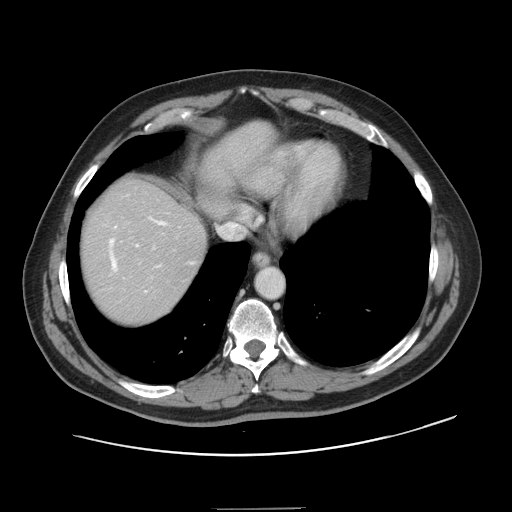
Contrast-enhanced abdominal CT, one axial slice; position 128 of 143 along the scan axis; 120 kVp; soft-tissue window (W 400 / L 40 HU); 2.5 mm slice thickness; 512 × 512 image matrix, field of view 402 × 402 mm. Male patient, age 62 years. Case-level facts recorded for this patient, not image findings: diagnosis: colorectal cancer liver metastases, imaged before liver resection.
Outlined on this slice (outlined manually by an expert reader):
- hepatic veins: bounding box <109,218,191,292> (left, top, right, bottom; pixels)
- liver: <81,122,272,324>
- planned liver remnant (the part of the liver to remain after resection): <80,122,272,299>